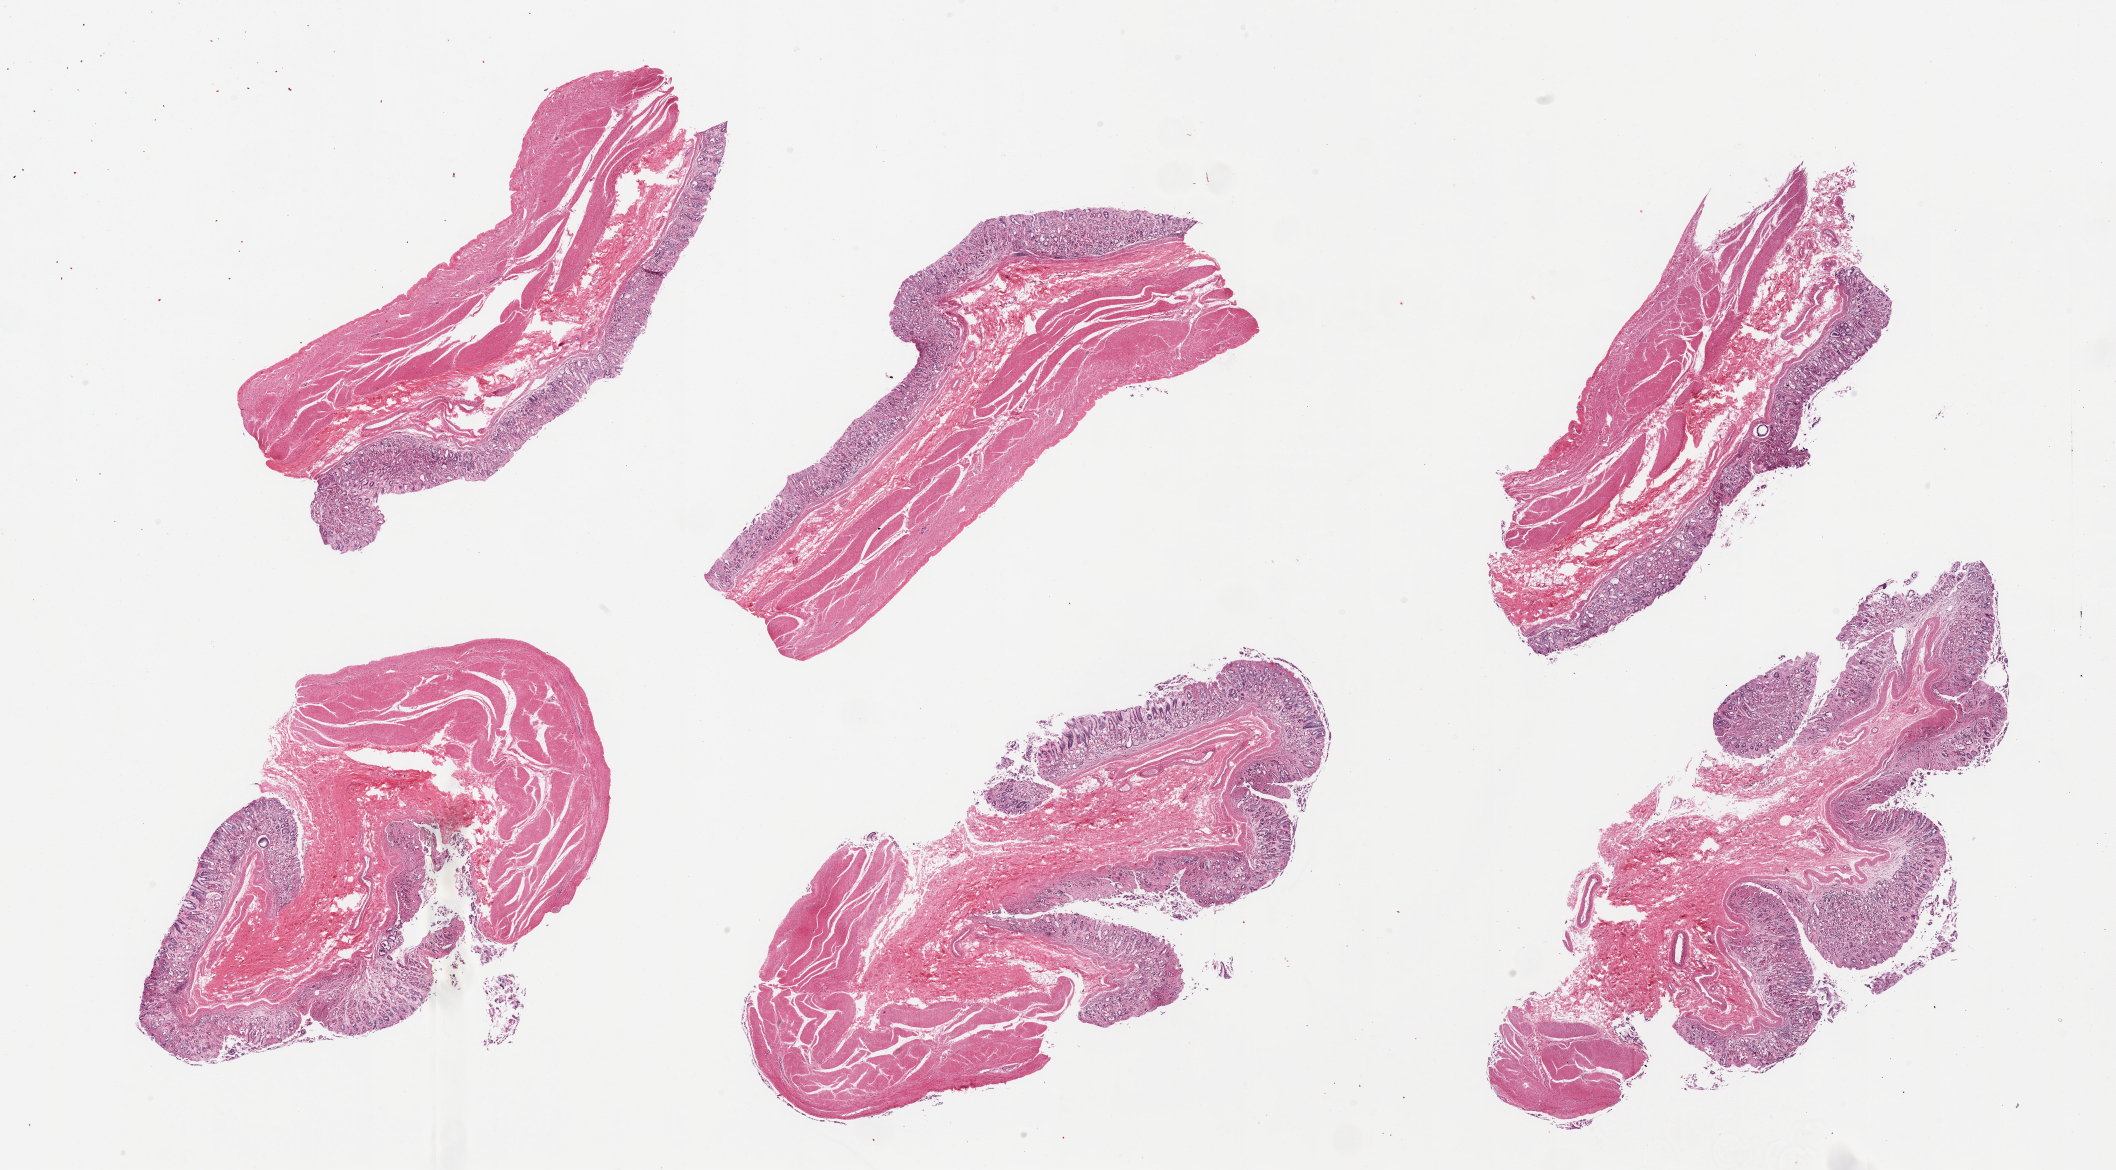
Digitized H&E-stained section, brightfield, low-resolution overview of the scanned area, about 33.5 x 18.5 mm; PAXgene-fixed paraffin-embedded (PFPE) section; sampled site (target tissue): stomach; donor tissue sample. Donor sex: male.
* reviewer comment on this tissue sample: 6 pieces; moderate to severe autolysis of mucosa and preserved muscularis